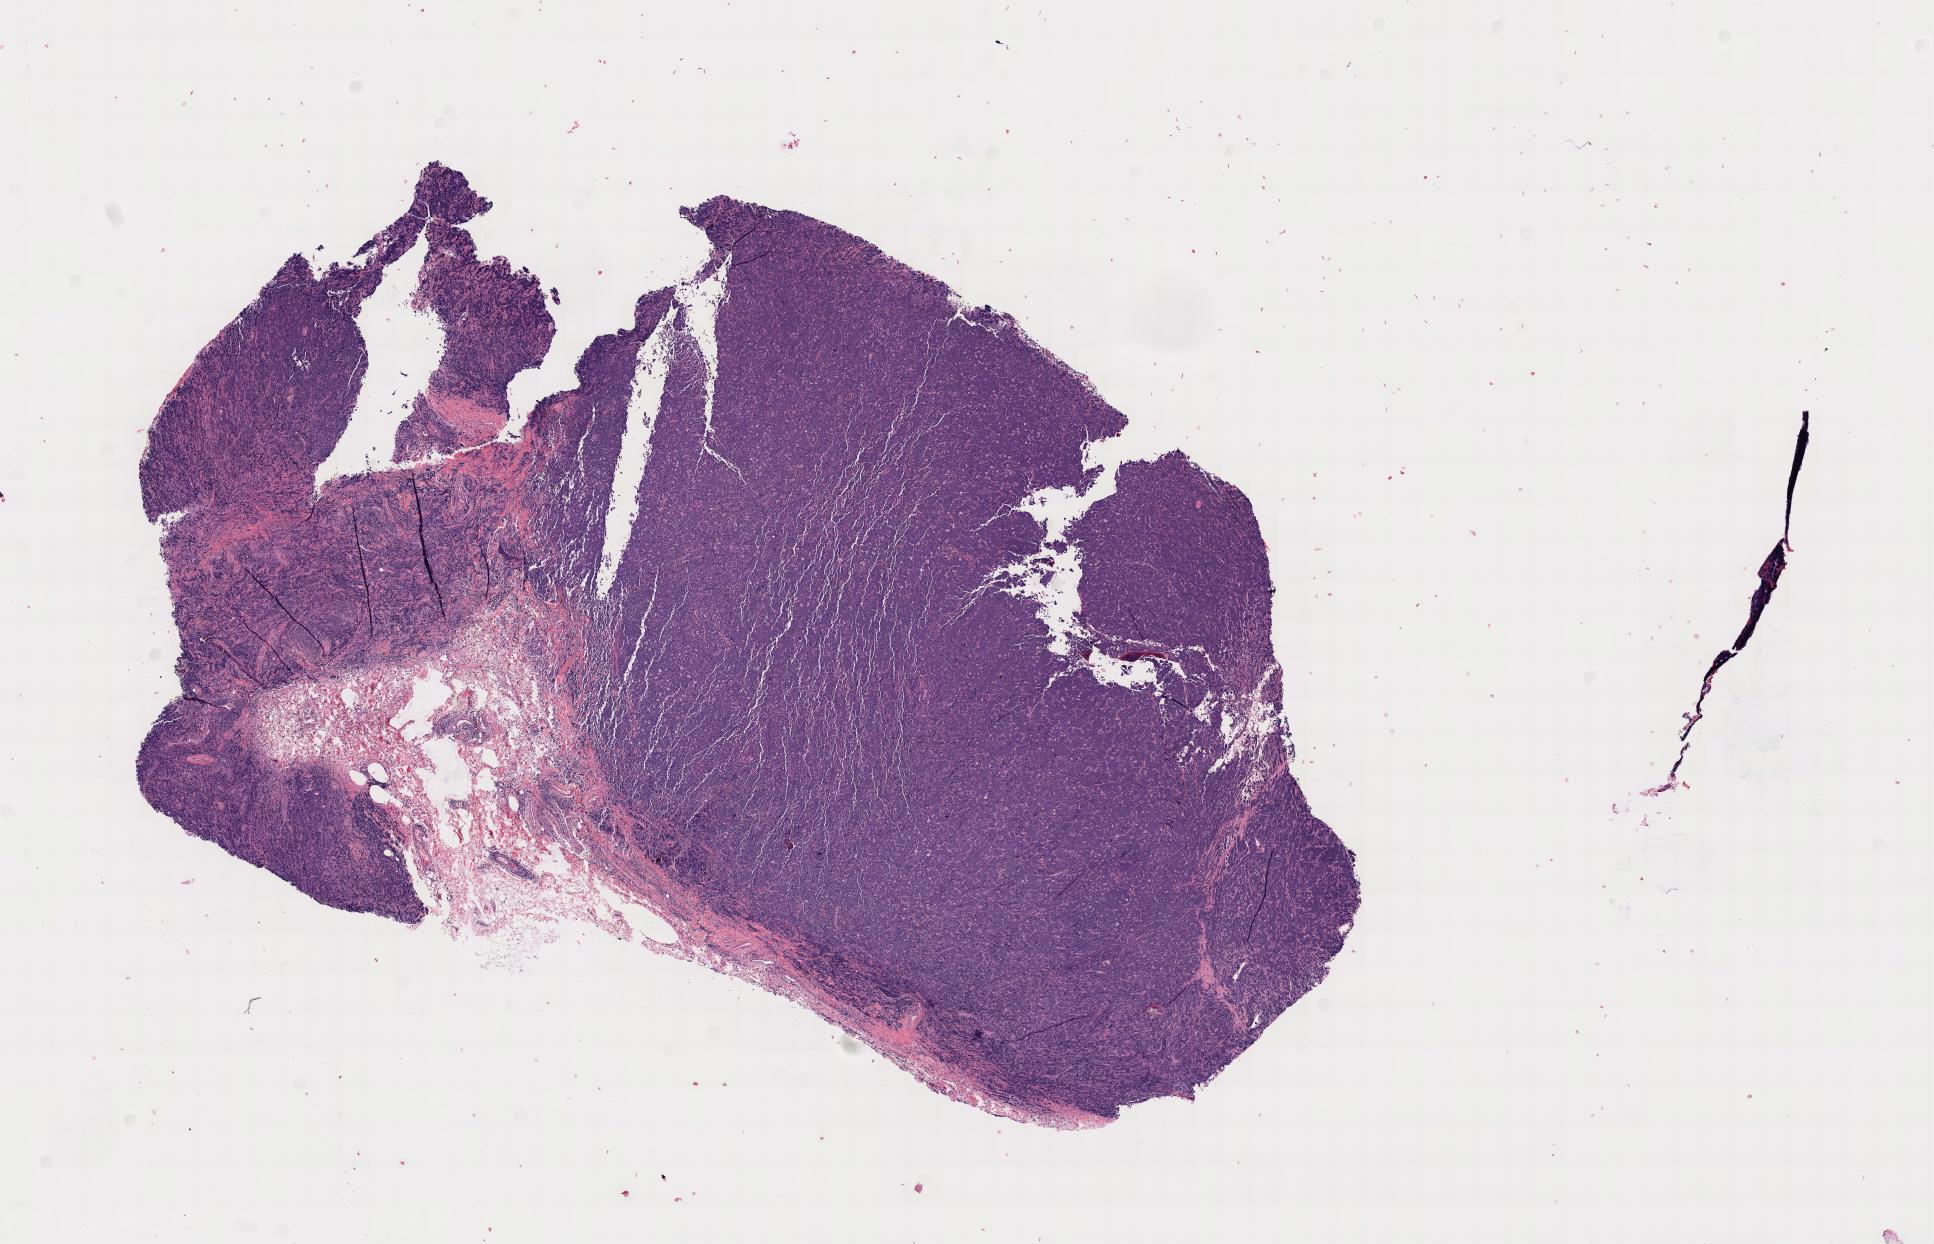
Whole-slide image, haematoxylin and eosin stain, shown as a low-resolution overview of the whole scanned area. Specimen: tumor tissue. Site: cranium. Patient: male, age at initial diagnosis 5 years.
Histologic diagnosis: Burkitt lymphoma, NOS.